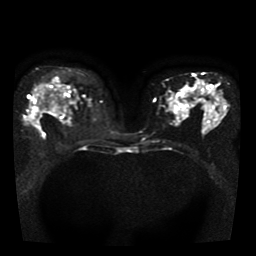
Breast MRI, one axial slice; position 23 of 41 along the scan axis; diffusion-weighted series; image 2 of 4 stored at this slice position (different b-values; order by instance number); 1.5 T; 5 mm slice thickness; 256 × 256 image matrix, field of view 330 × 330 mm. Female patient.
Structures marked on this image (expert manual segmentation):
- tumour on diffusion-weighted imaging: bounding box (x1, y1, x2, y2) in pixels: (30, 89, 46, 123)